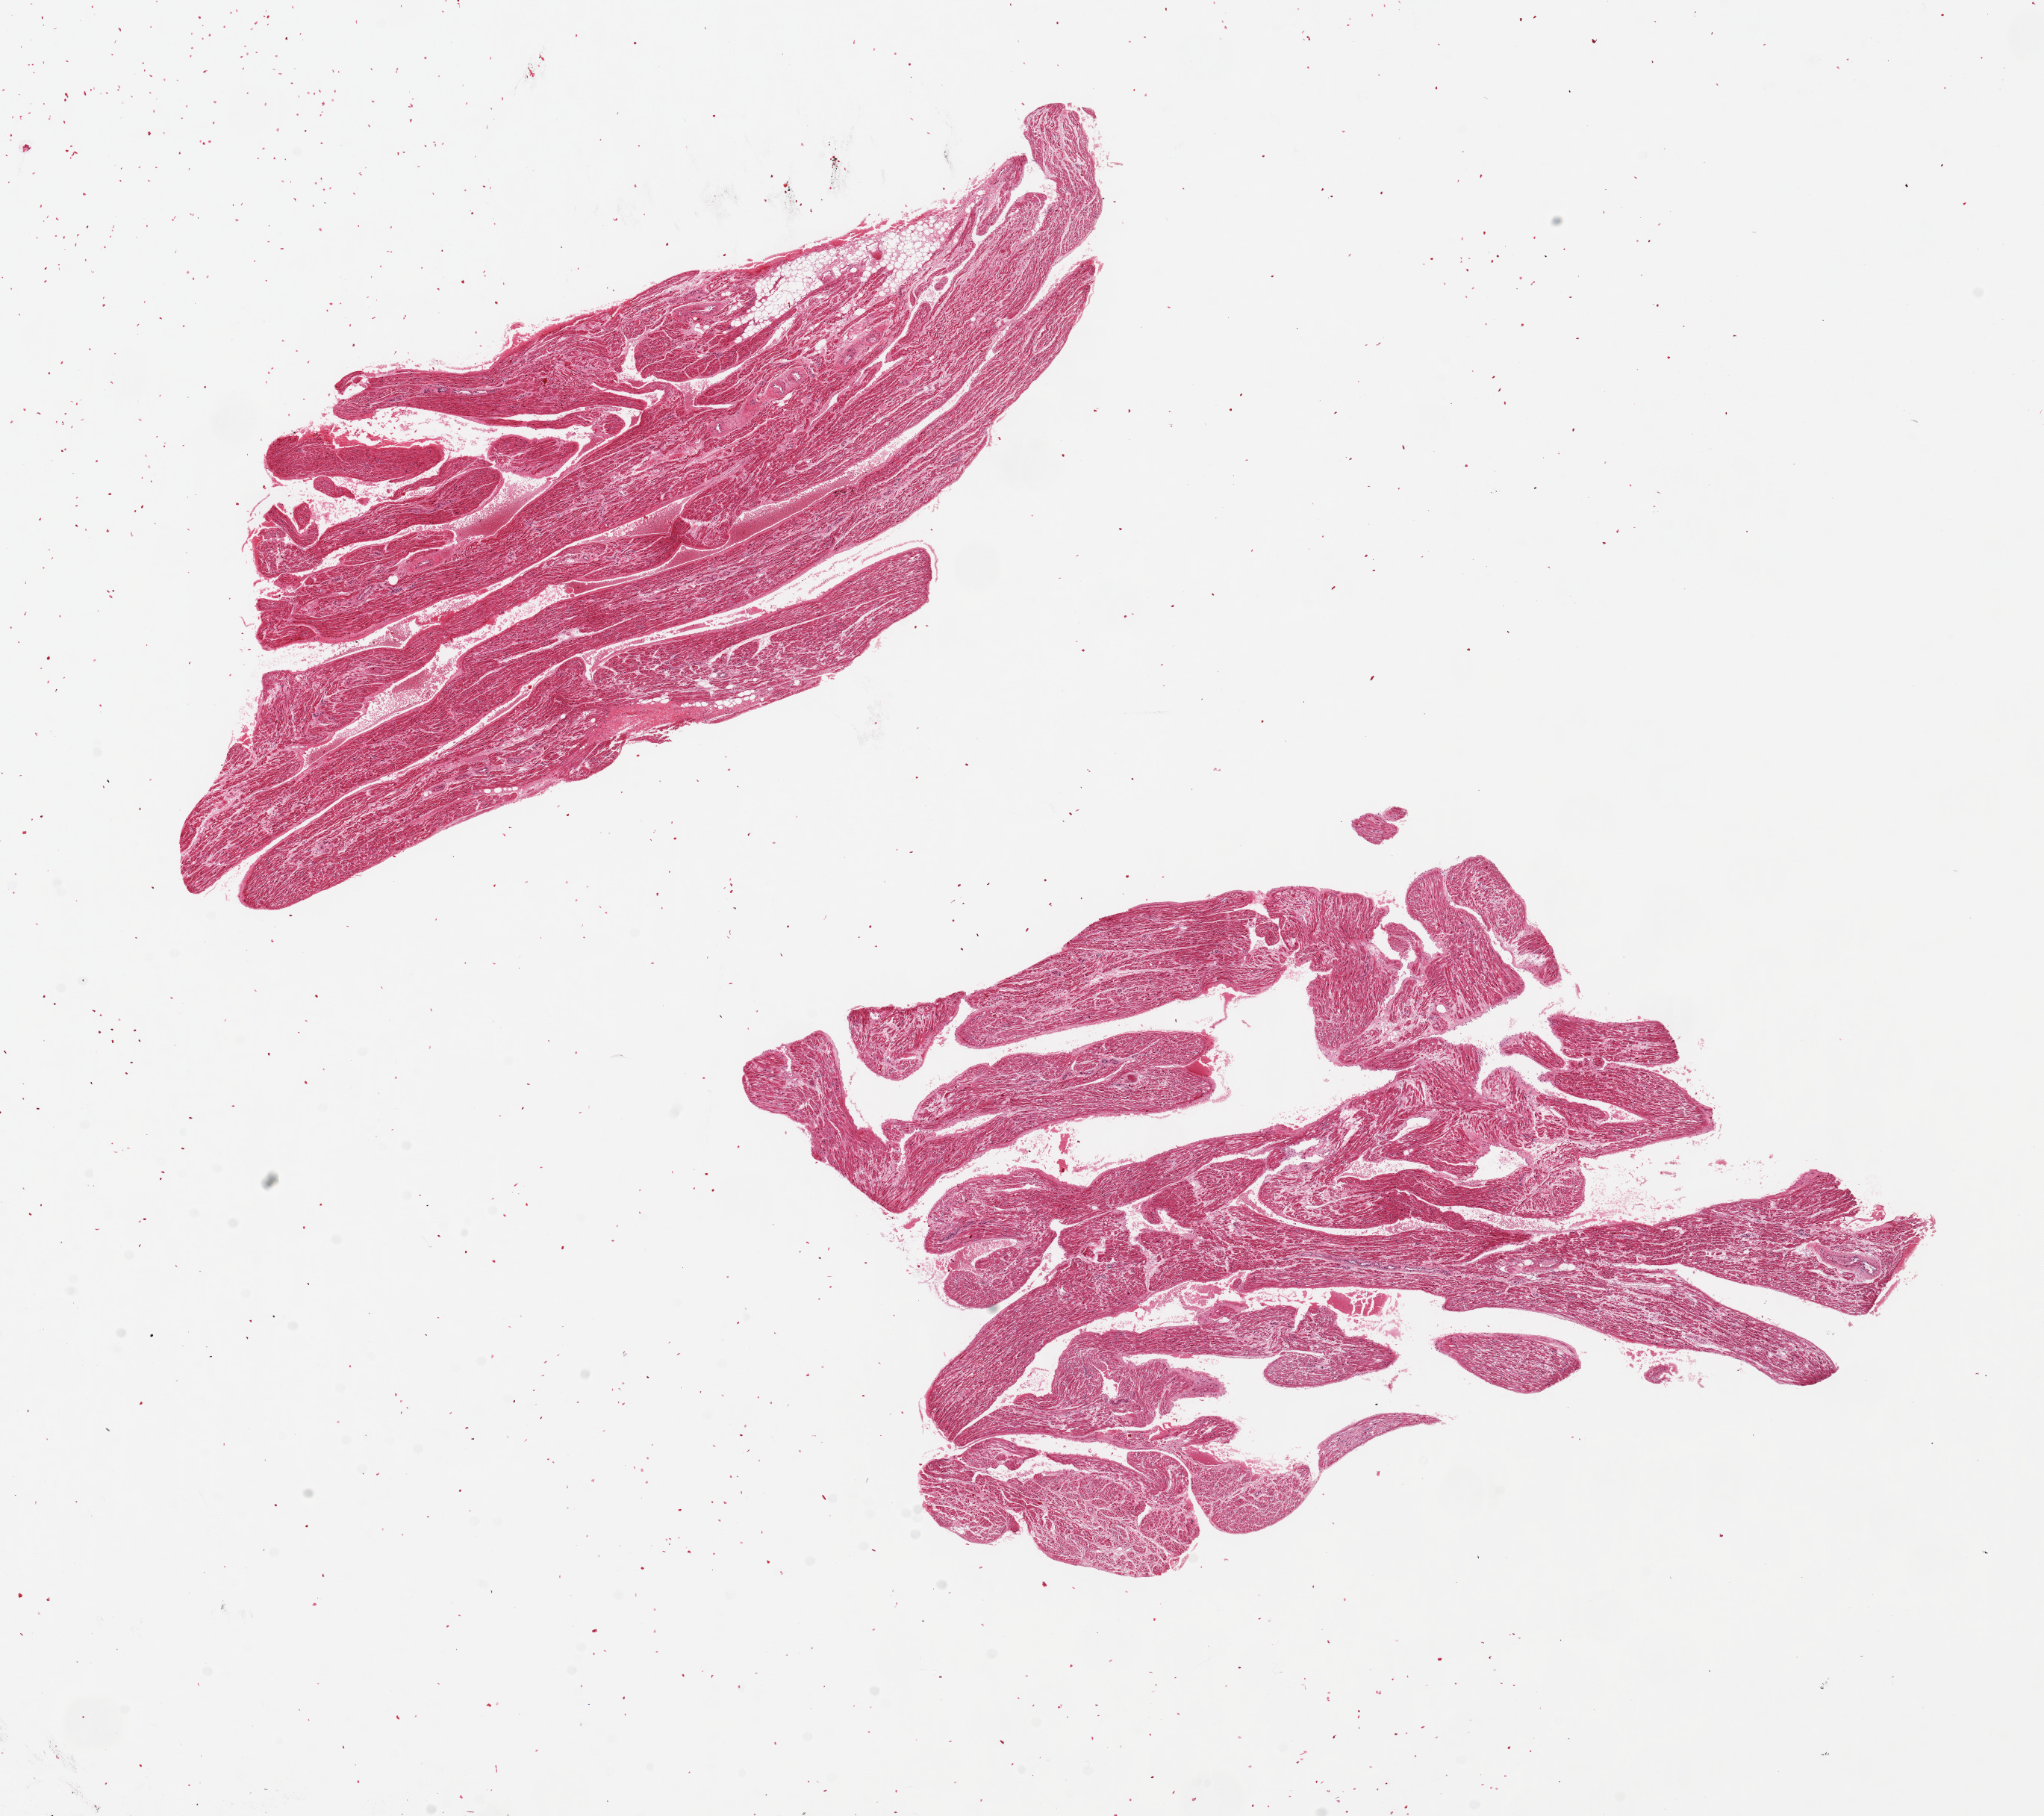
Whole-slide image, hematoxylin and eosin (H&E) stain, shown as a low-resolution overview of the whole scanned area (about 21.7 x 19.2 mm, from a 20x scan); PAXgene-fixed paraffin-embedded (PFPE) section; target tissue: auricular appendage; donor tissue sample. Female donor.
• reviewer comment on this tissue sample: 2 pieces ~9x6mm